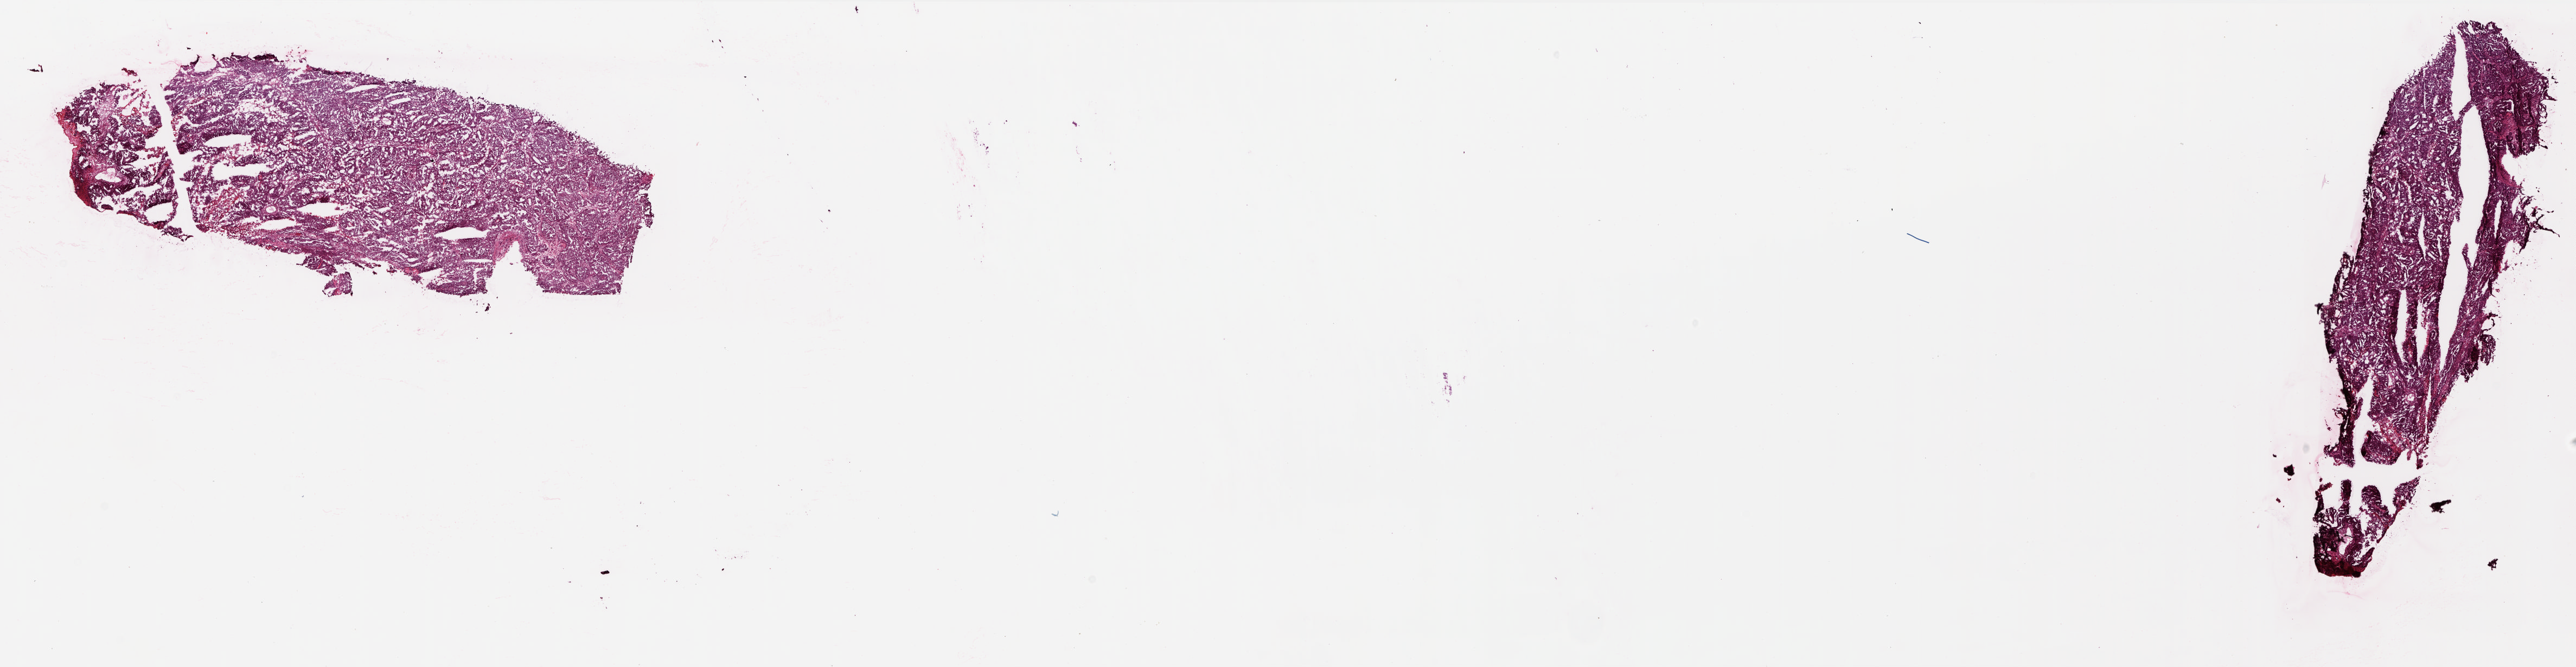
H&E-stained whole-slide image — a low-resolution overview of the entire scanned area, about 37.9 x 9.8 mm (acquisition: 20x scan), frozen section from the top of the tissue portion, ovary, primary tumour sample. Female patient; age at initial diagnosis 85 years. Histologic grade: G3 (poorly differentiated). Composition of this section per pathologist review: tumour cells 75%, tumour nuclei 80%, stromal cells 22%, necrosis 3%.
- diagnosis: Serous cystadenocarcinoma, NOS